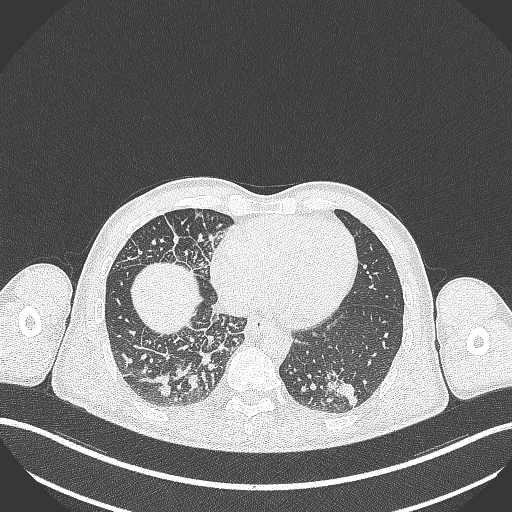
Chest CT, one axial slice. Position 93 of 348 along the scan axis. Reconstruction kernel B70f. 120 kVp. Lung window (W 1500 / L -600 HU). 1 mm slice thickness. 512 × 512 image matrix, field of view 400 × 400 mm. Male patient, age 49 years. Case-level facts recorded for this patient, not image findings: clinical TNM (as recorded): T2b N1 M0.
Structures marked on this image (rectangle marked by the reading radiologist):
- lung tumour (recorded histology: adenocarcinoma): box from (x=317, y=366) to (x=365, y=413) px